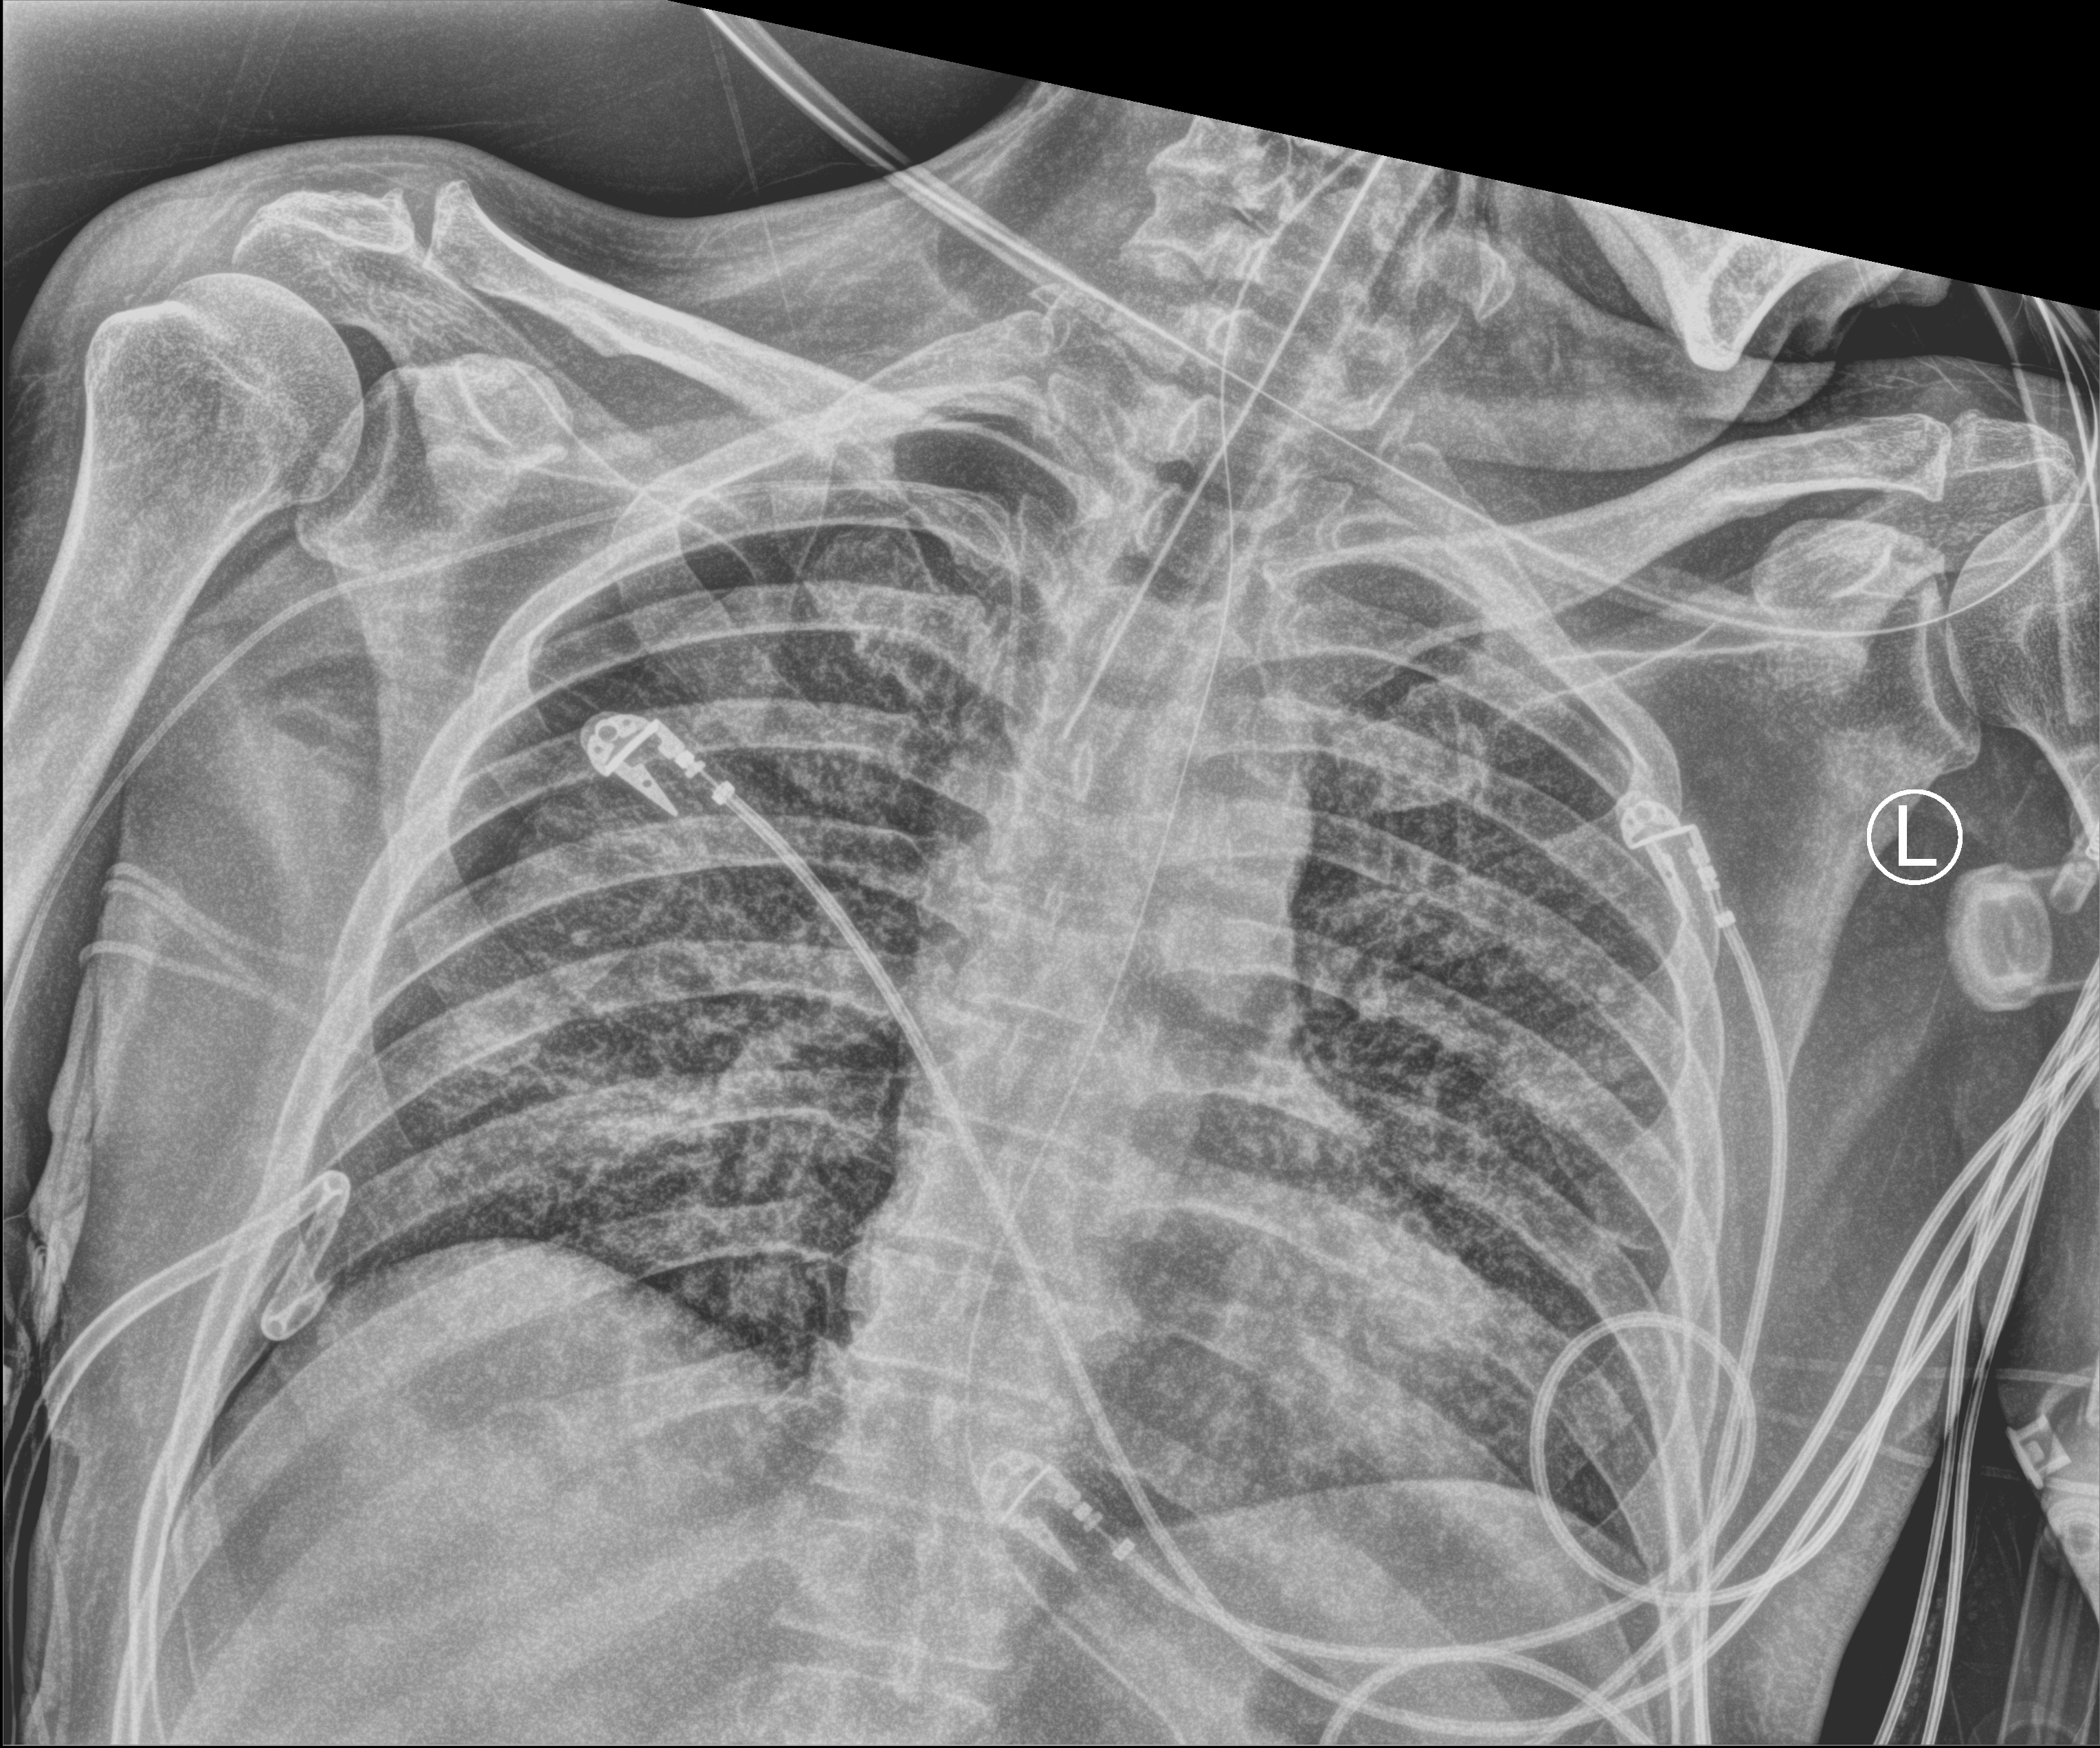
Portable chest radiograph; anteroposterior (AP) projection. Male patient hospitalised with COVID-19, age 18–59 years.
Admission-level facts for this patient (not findings on this image; timing relative to this image not recorded): mechanically ventilated during this hospital stay: yes; length of hospital stay: 77 days.